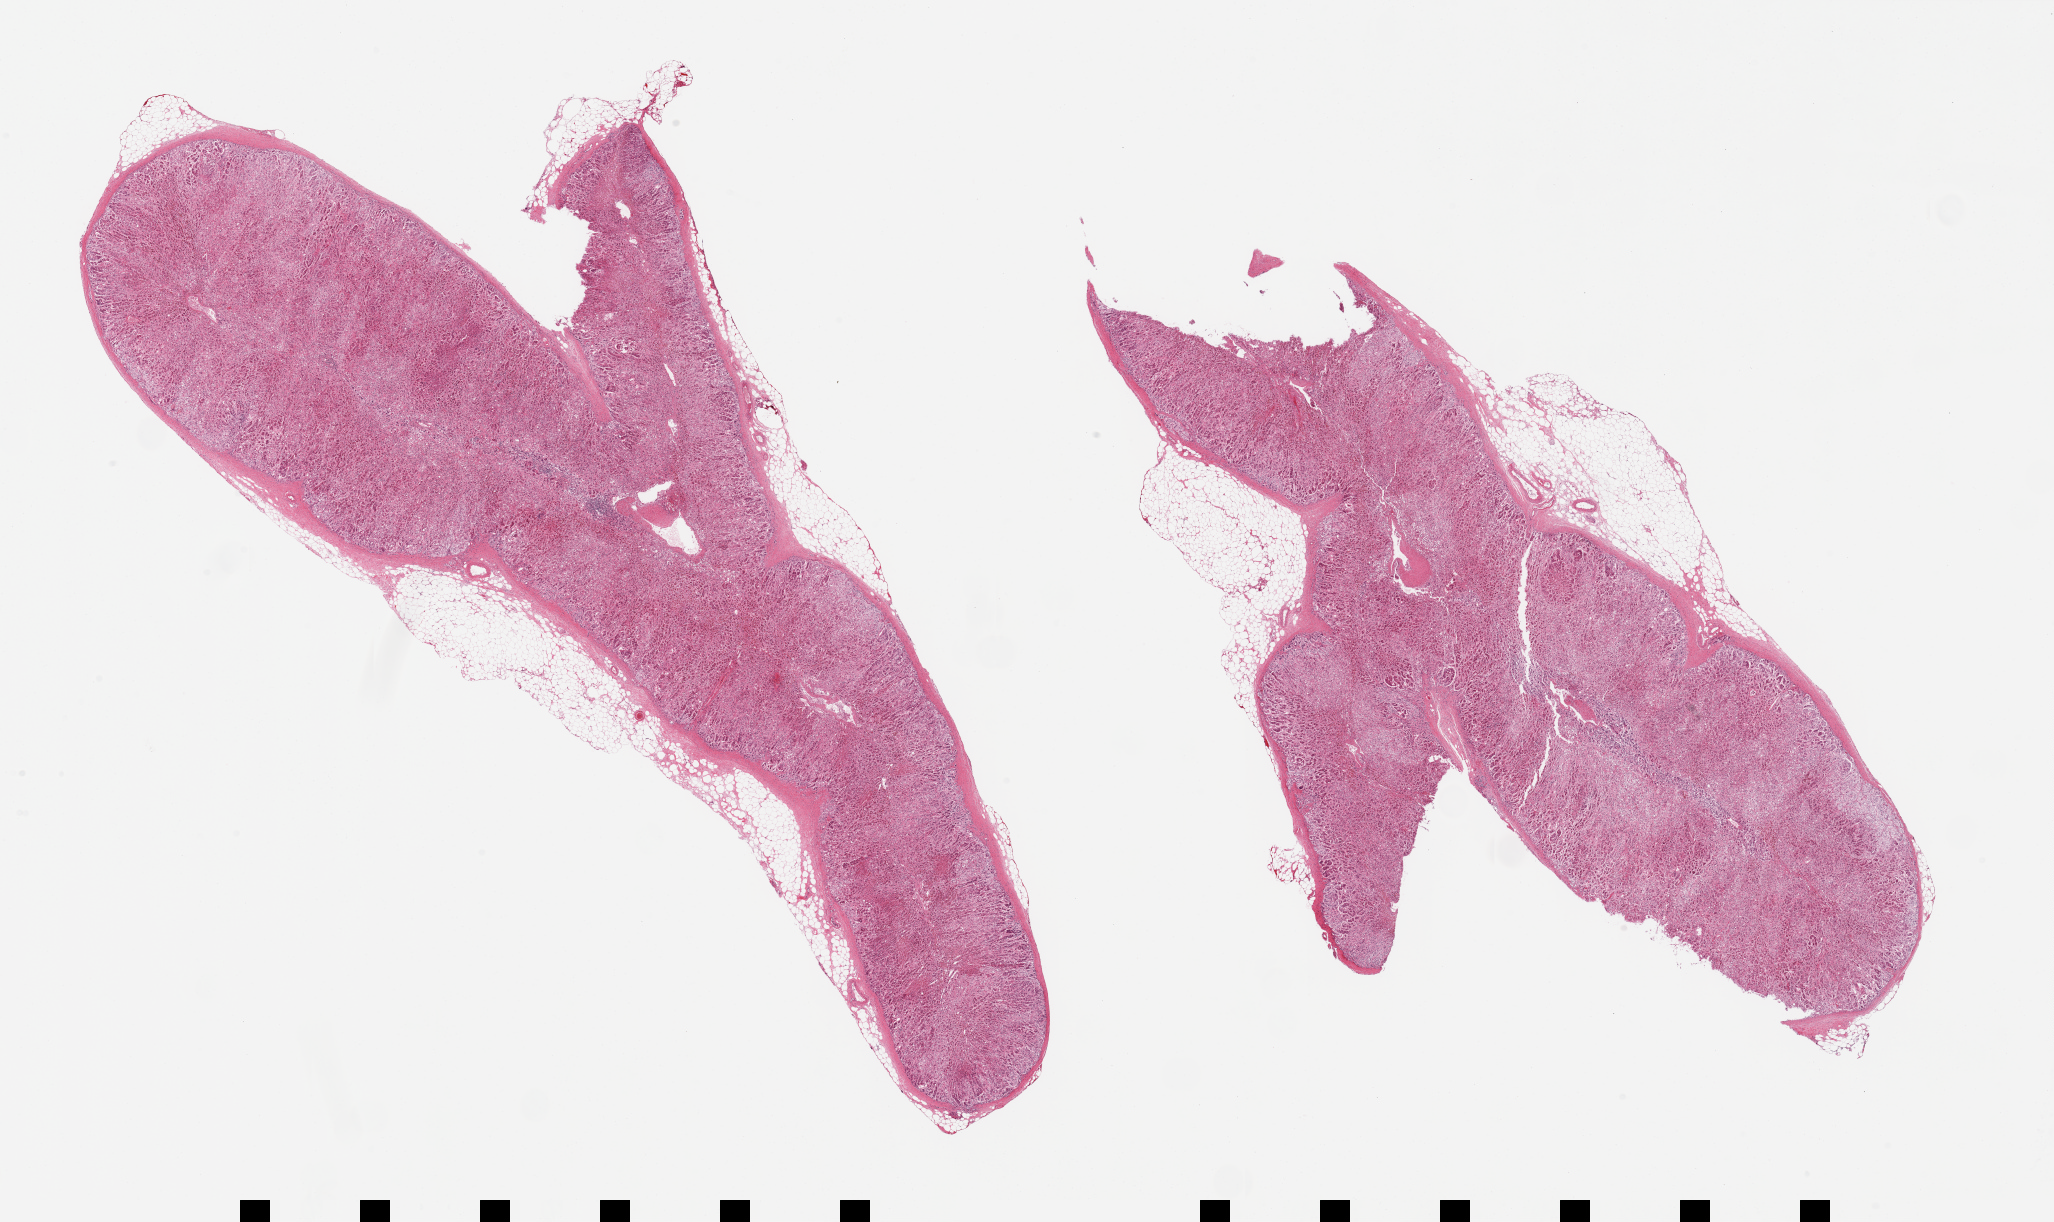
Digitized H&E-stained section, brightfield — a low-resolution overview of the entire scanned area, about 32.5 x 19.3 mm. PAXgene-fixed, paraffin-embedded tissue. Section of adrenal gland (target tissue). Donor tissue sample. Donor sex: male.
Pathologist's review note for this sample: 2 pieces, advanced autolysis, all cortex, adherent fatty nubbins up to ~1.5mm.